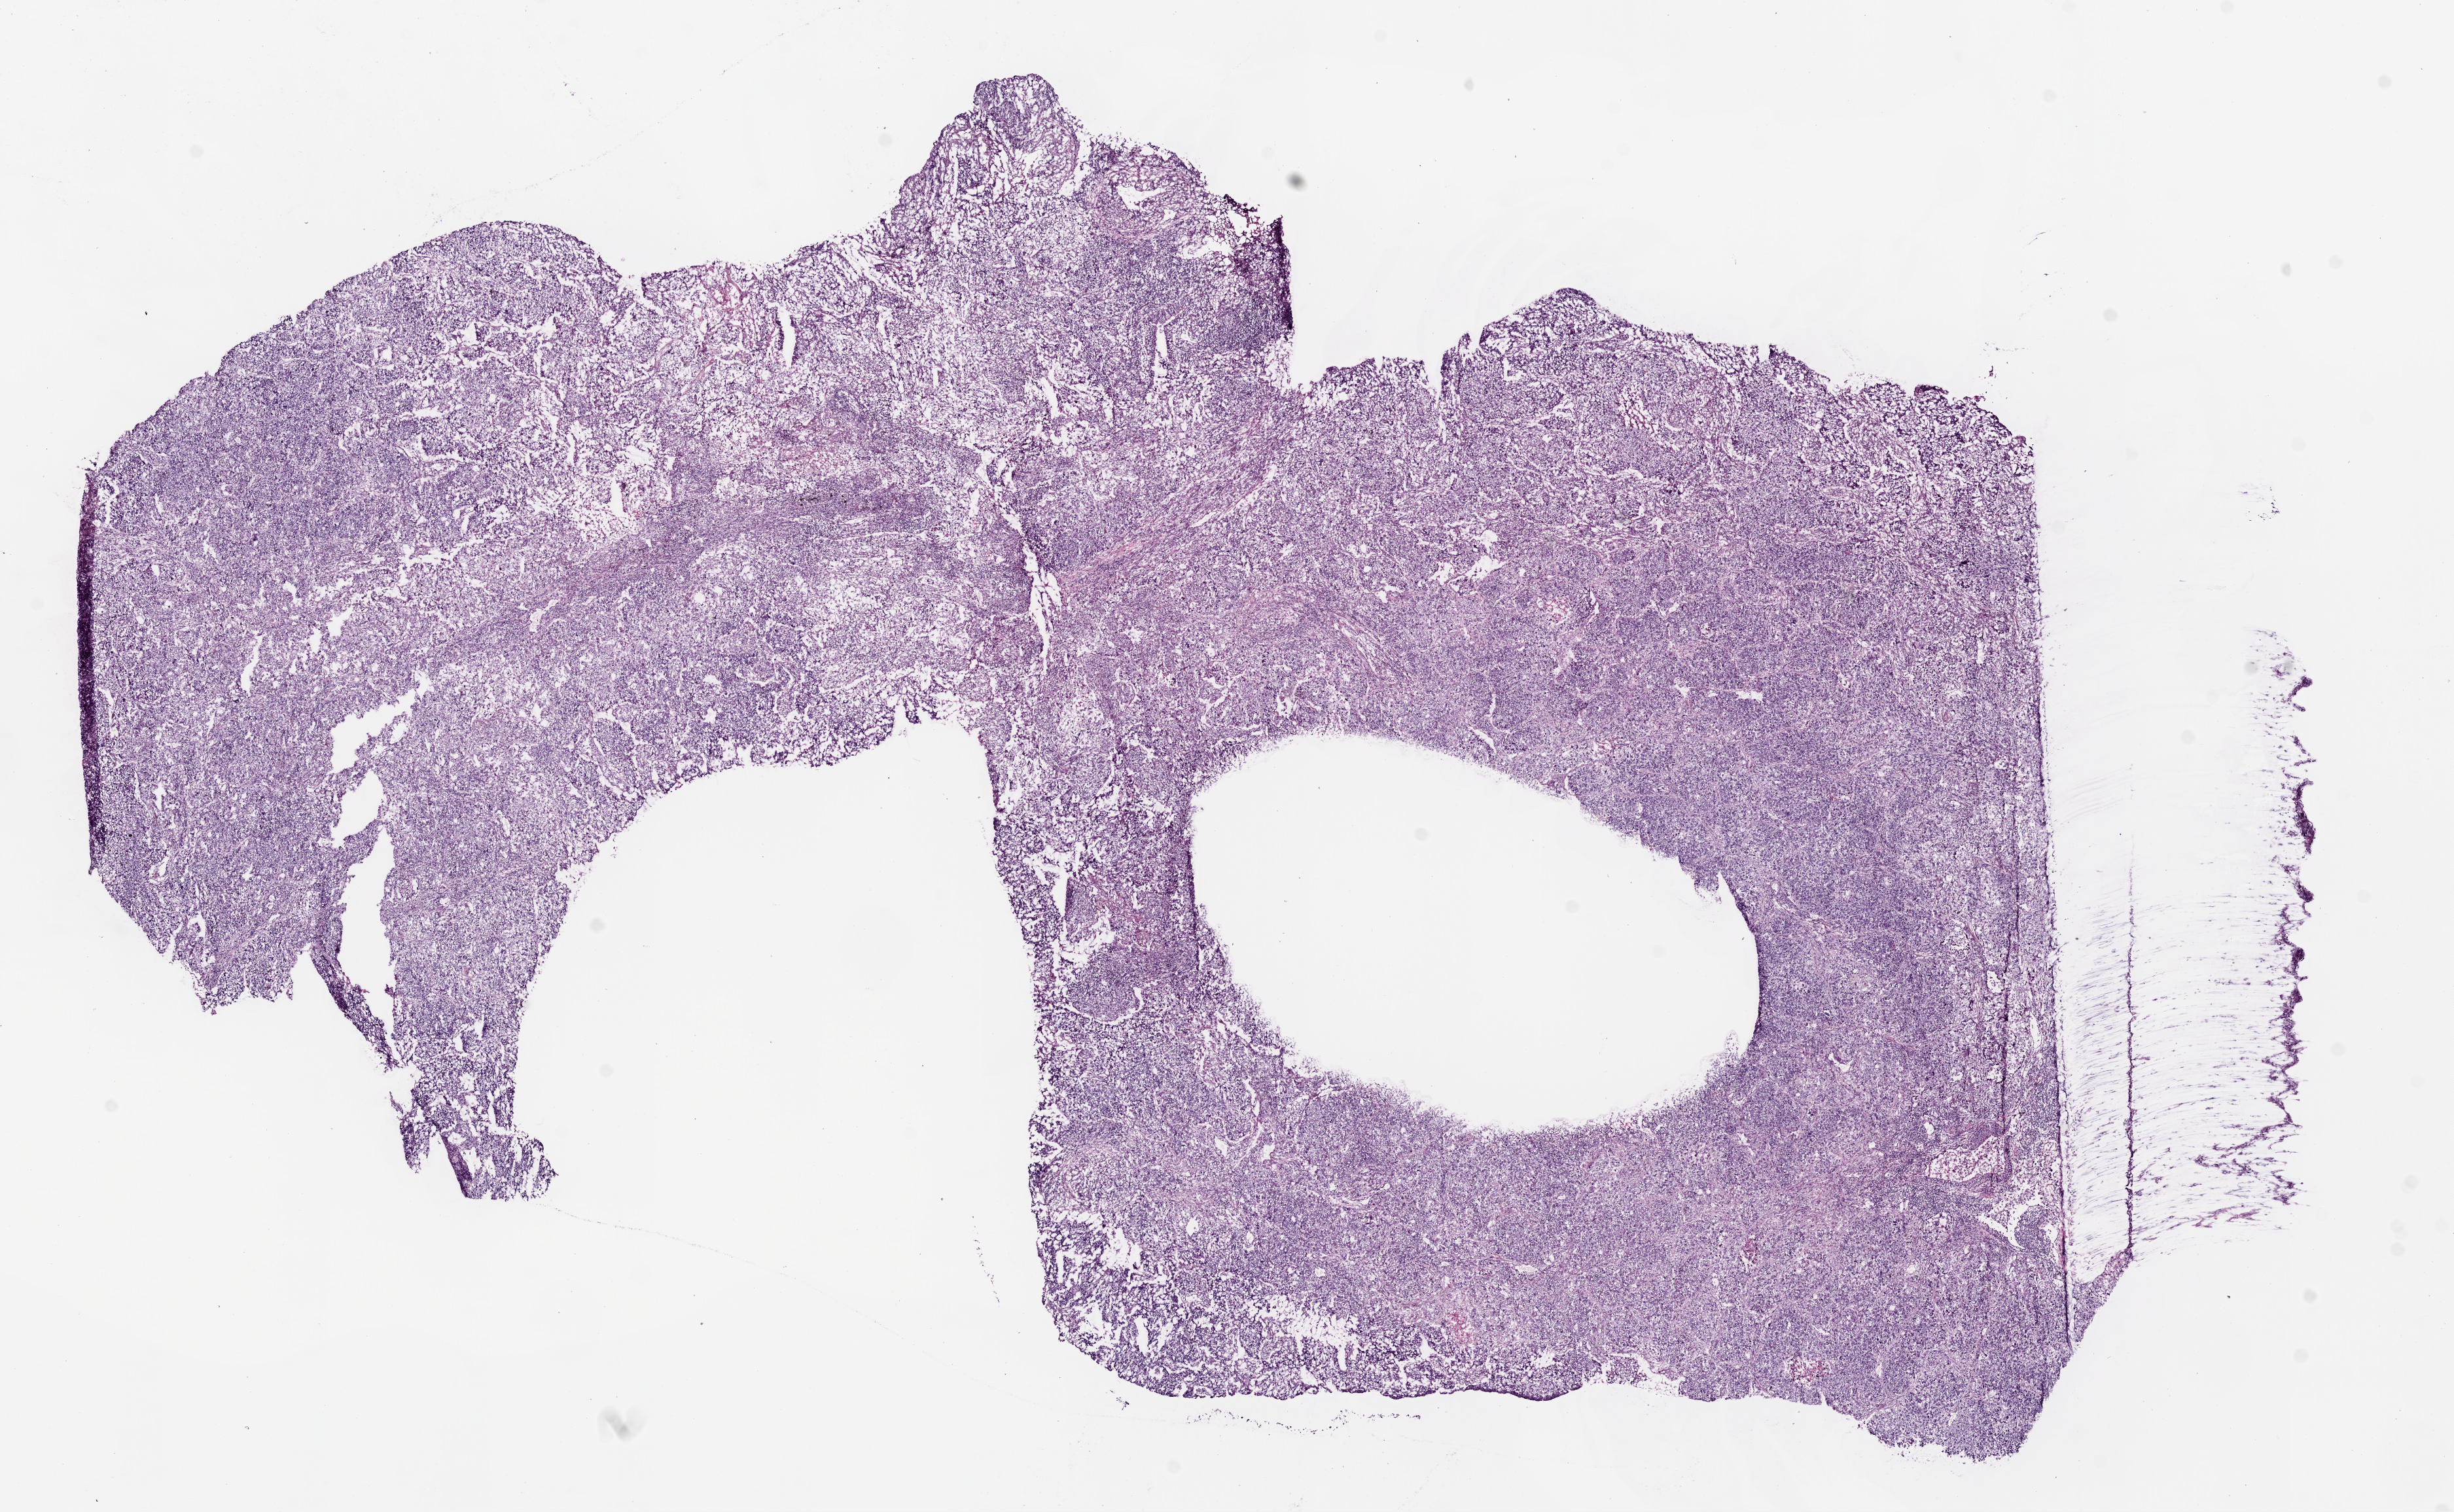
Whole-slide histology image, H&E-stained — low-resolution overview of the scanned area, about 15.0 x 9.3 mm. Frozen section. Lung, primary tumour sample. Patient: female, age at initial diagnosis 65 years. Pathologist review of this section (percent, as recorded): tumour cells 86%, tumour nuclei 70%, normal cells 2%, stromal cells 10%, necrosis 2%.
AJCC pathologic stage: IIB. Pathologic diagnosis: Adenocarcinoma with mixed subtypes (upper lobe, lung). TNM: T2 N1 M0.